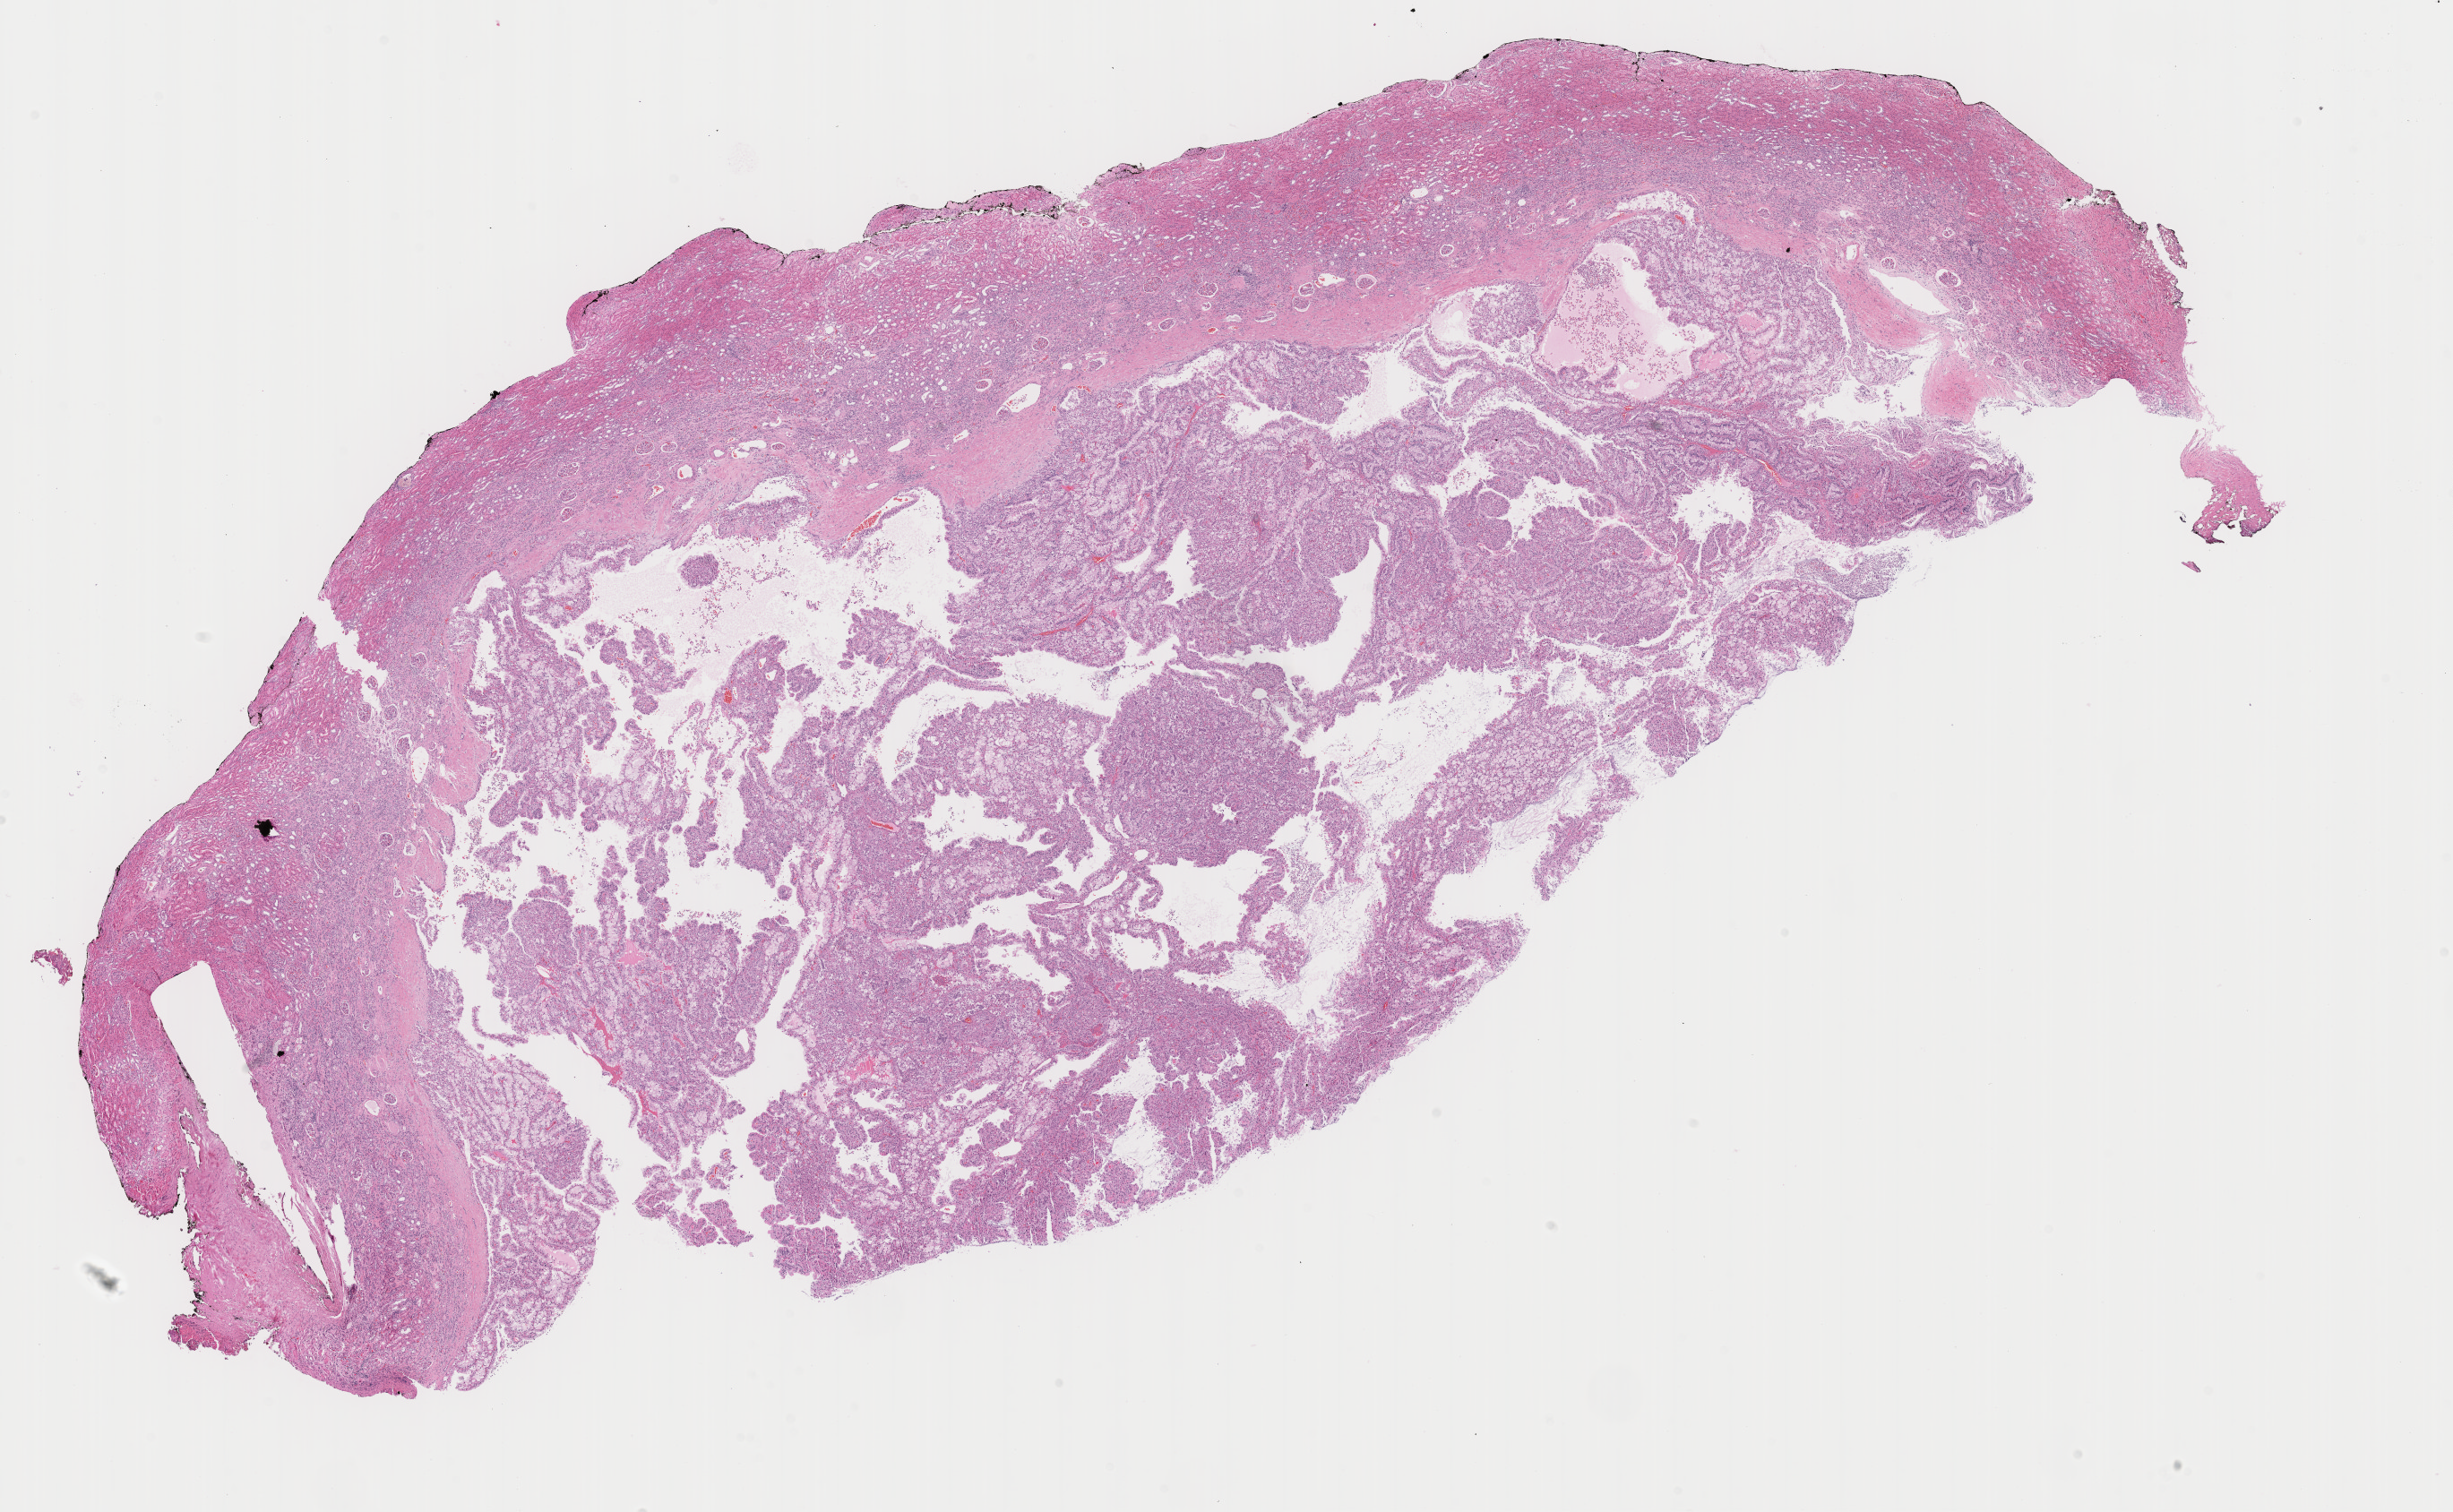
Whole-slide histology image, H&E, whole scanned area (about 22.1 x 13.7 mm, from a 40x scan) shown as a low-resolution overview. Formalin-fixed paraffin-embedded (FFPE) diagnostic section. Kidney, primary tumour sample. Patient: female, age at initial diagnosis 60 years.
• histologic diagnosis: Papillary adenocarcinoma, NOS
• AJCC pathologic stage: I
• TNM: T1a NX MX
• laterality: right